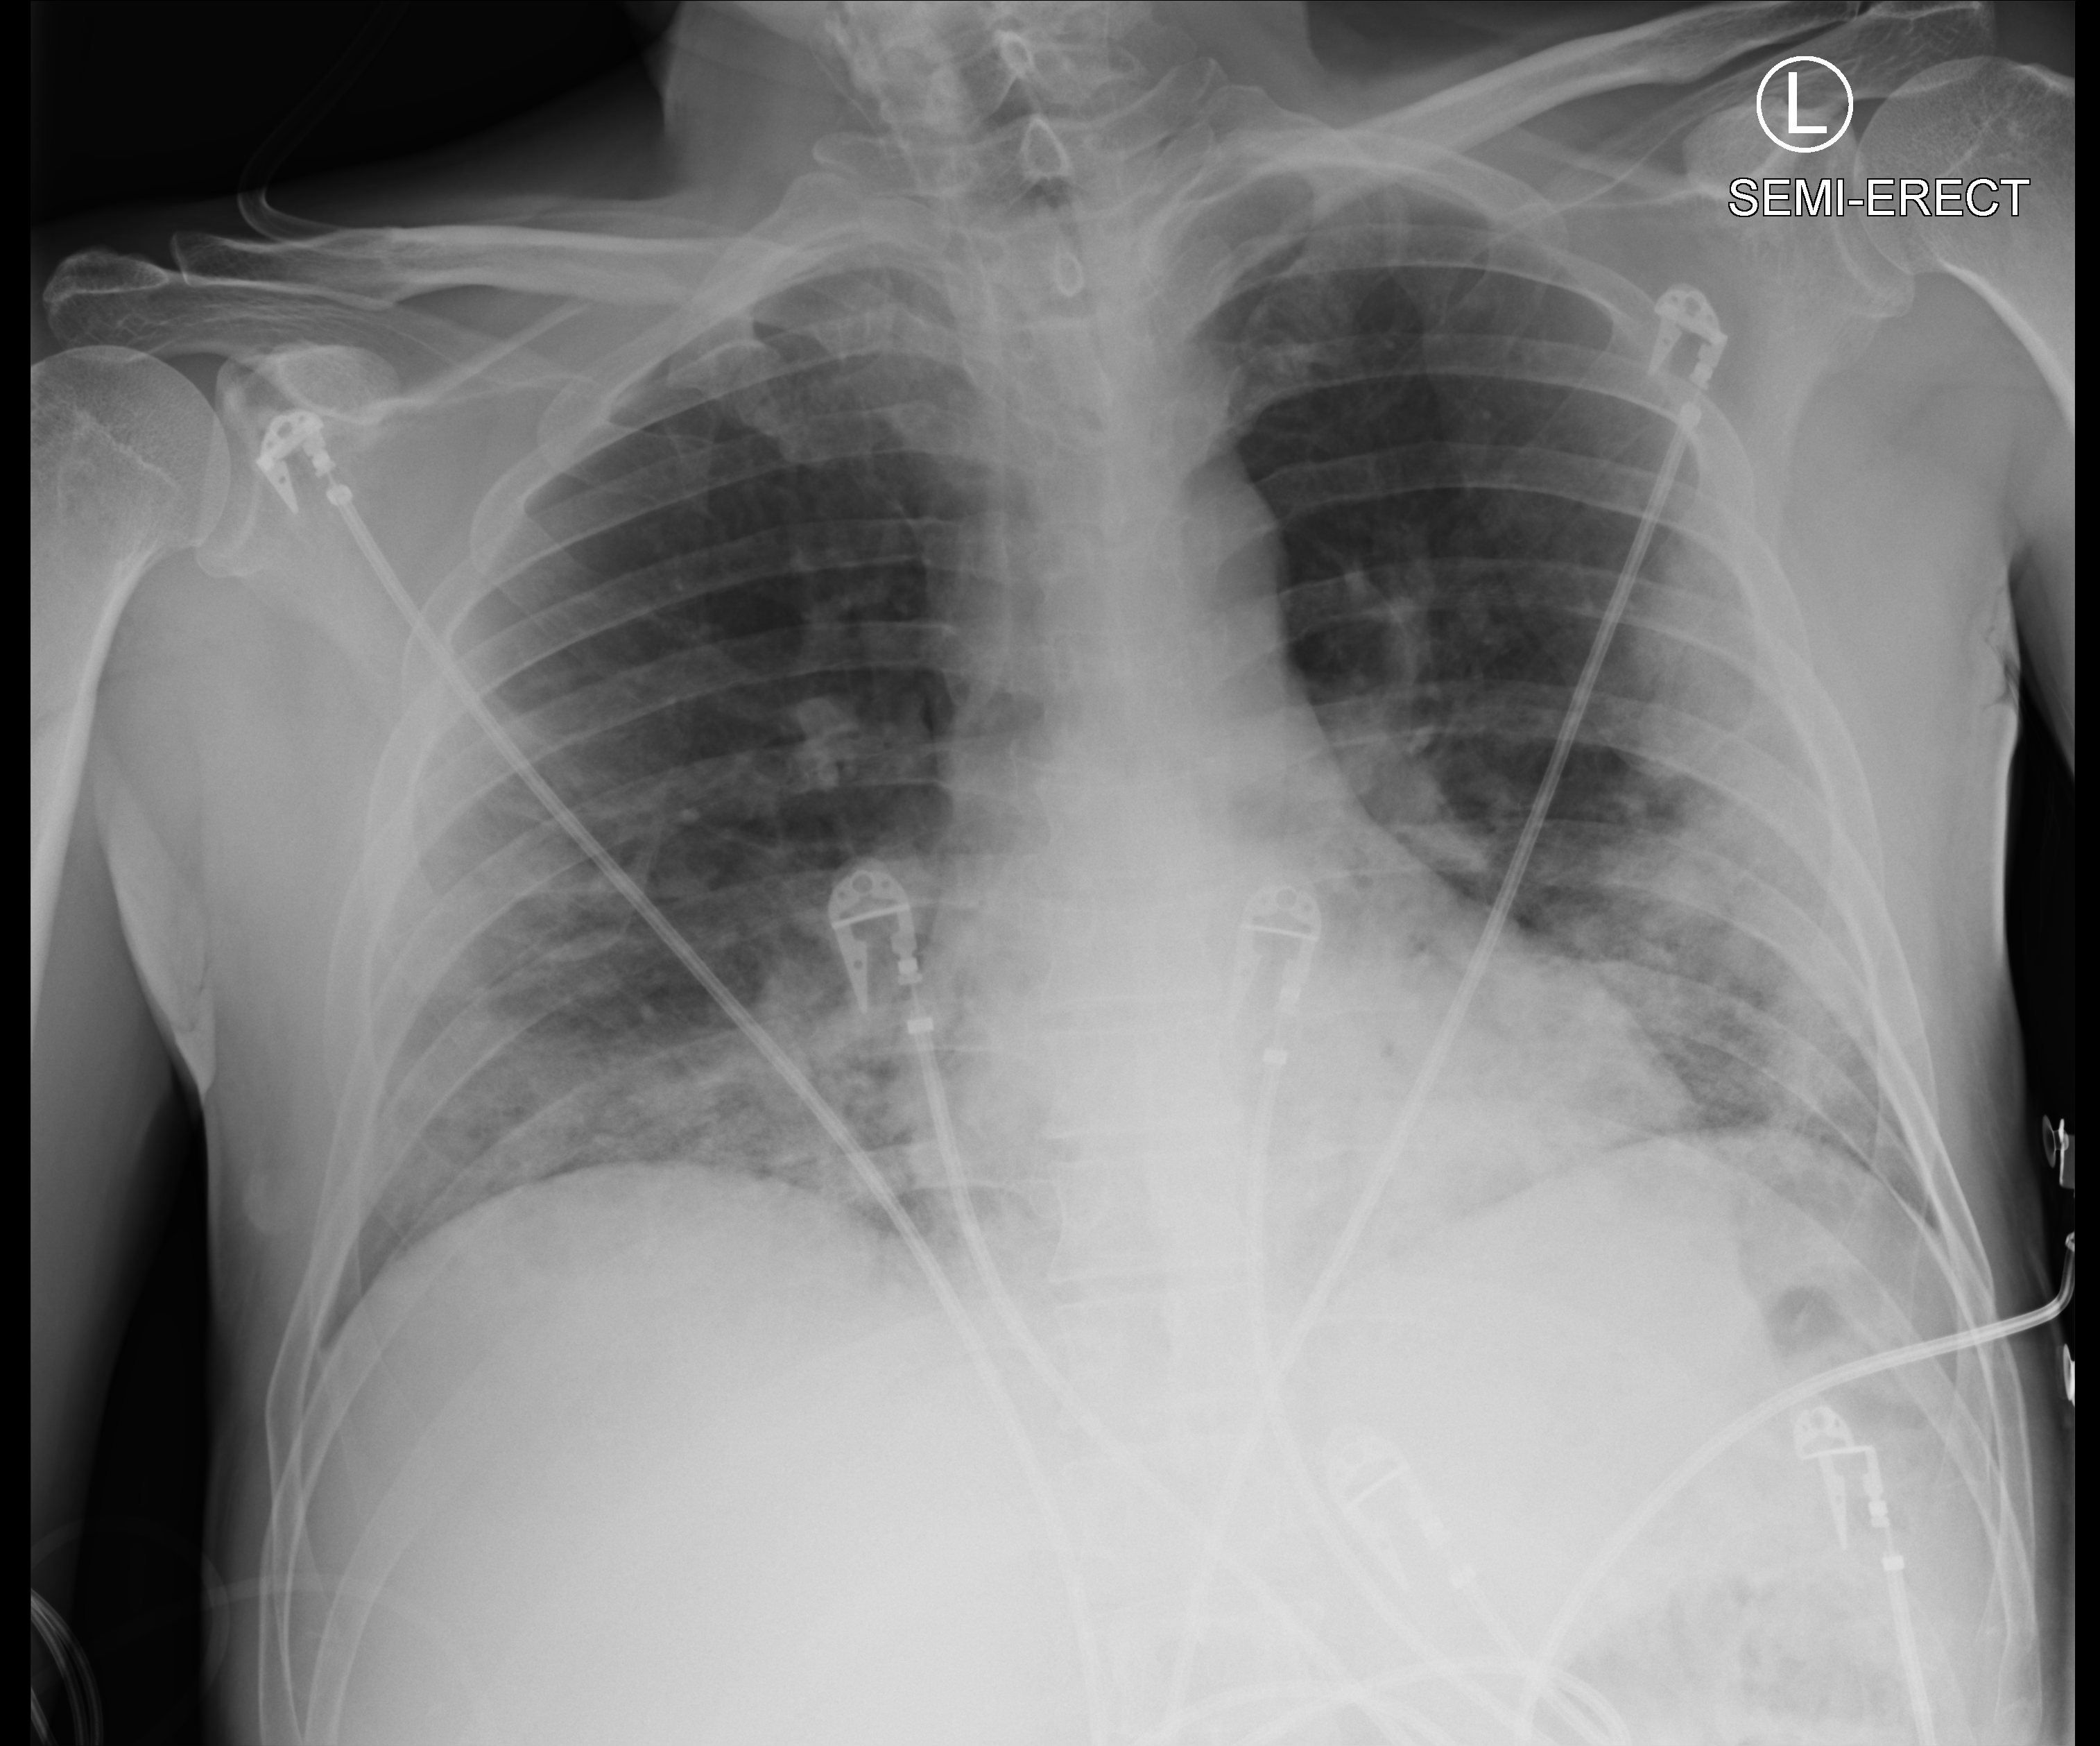
Bedside chest radiograph (computed radiography), anteroposterior (AP) projection. Male patient hospitalised with COVID-19, age 18–59 years.
Admission-level facts for this patient (not findings on this image; timing relative to this image not recorded): mechanically ventilated during this hospital stay: yes; diabetes (admission record): yes.